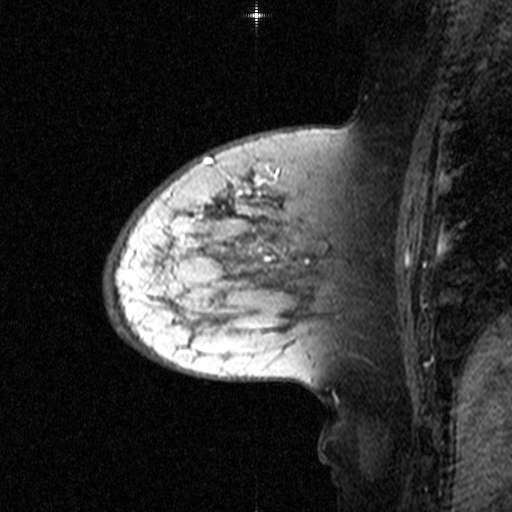
Breast MRI (dynamic contrast-enhanced), one sagittal slice. Position 17 of 44 along the scan axis. Dynamic contrast-enhanced study with each time point stored as its own series, time point 2 of 3 at this slice position (early post-contrast, ordered by acquisition time). 1.5 T. TE 4.5 ms, TR 11 ms. 3 mm slice thickness. 512 × 512 image matrix. Female patient, age 65 years. From the clinical record (not read from this slice): setting: breast cancer imaged before/during neoadjuvant chemotherapy; receptor status: HER2-positive.
Outlined on this slice (semi-automatic segmentation, software-assisted and operator-edited):
- analysis volume of interest (the breast-tissue region the enhancement analysis was run in; not a lesion): box from (x=160, y=172) to (x=329, y=345) px
- tumour enhancement mask (voxels above the 90 % enhancement threshold inside the analysis volume of interest): (x=173, y=174)–(x=277, y=260)